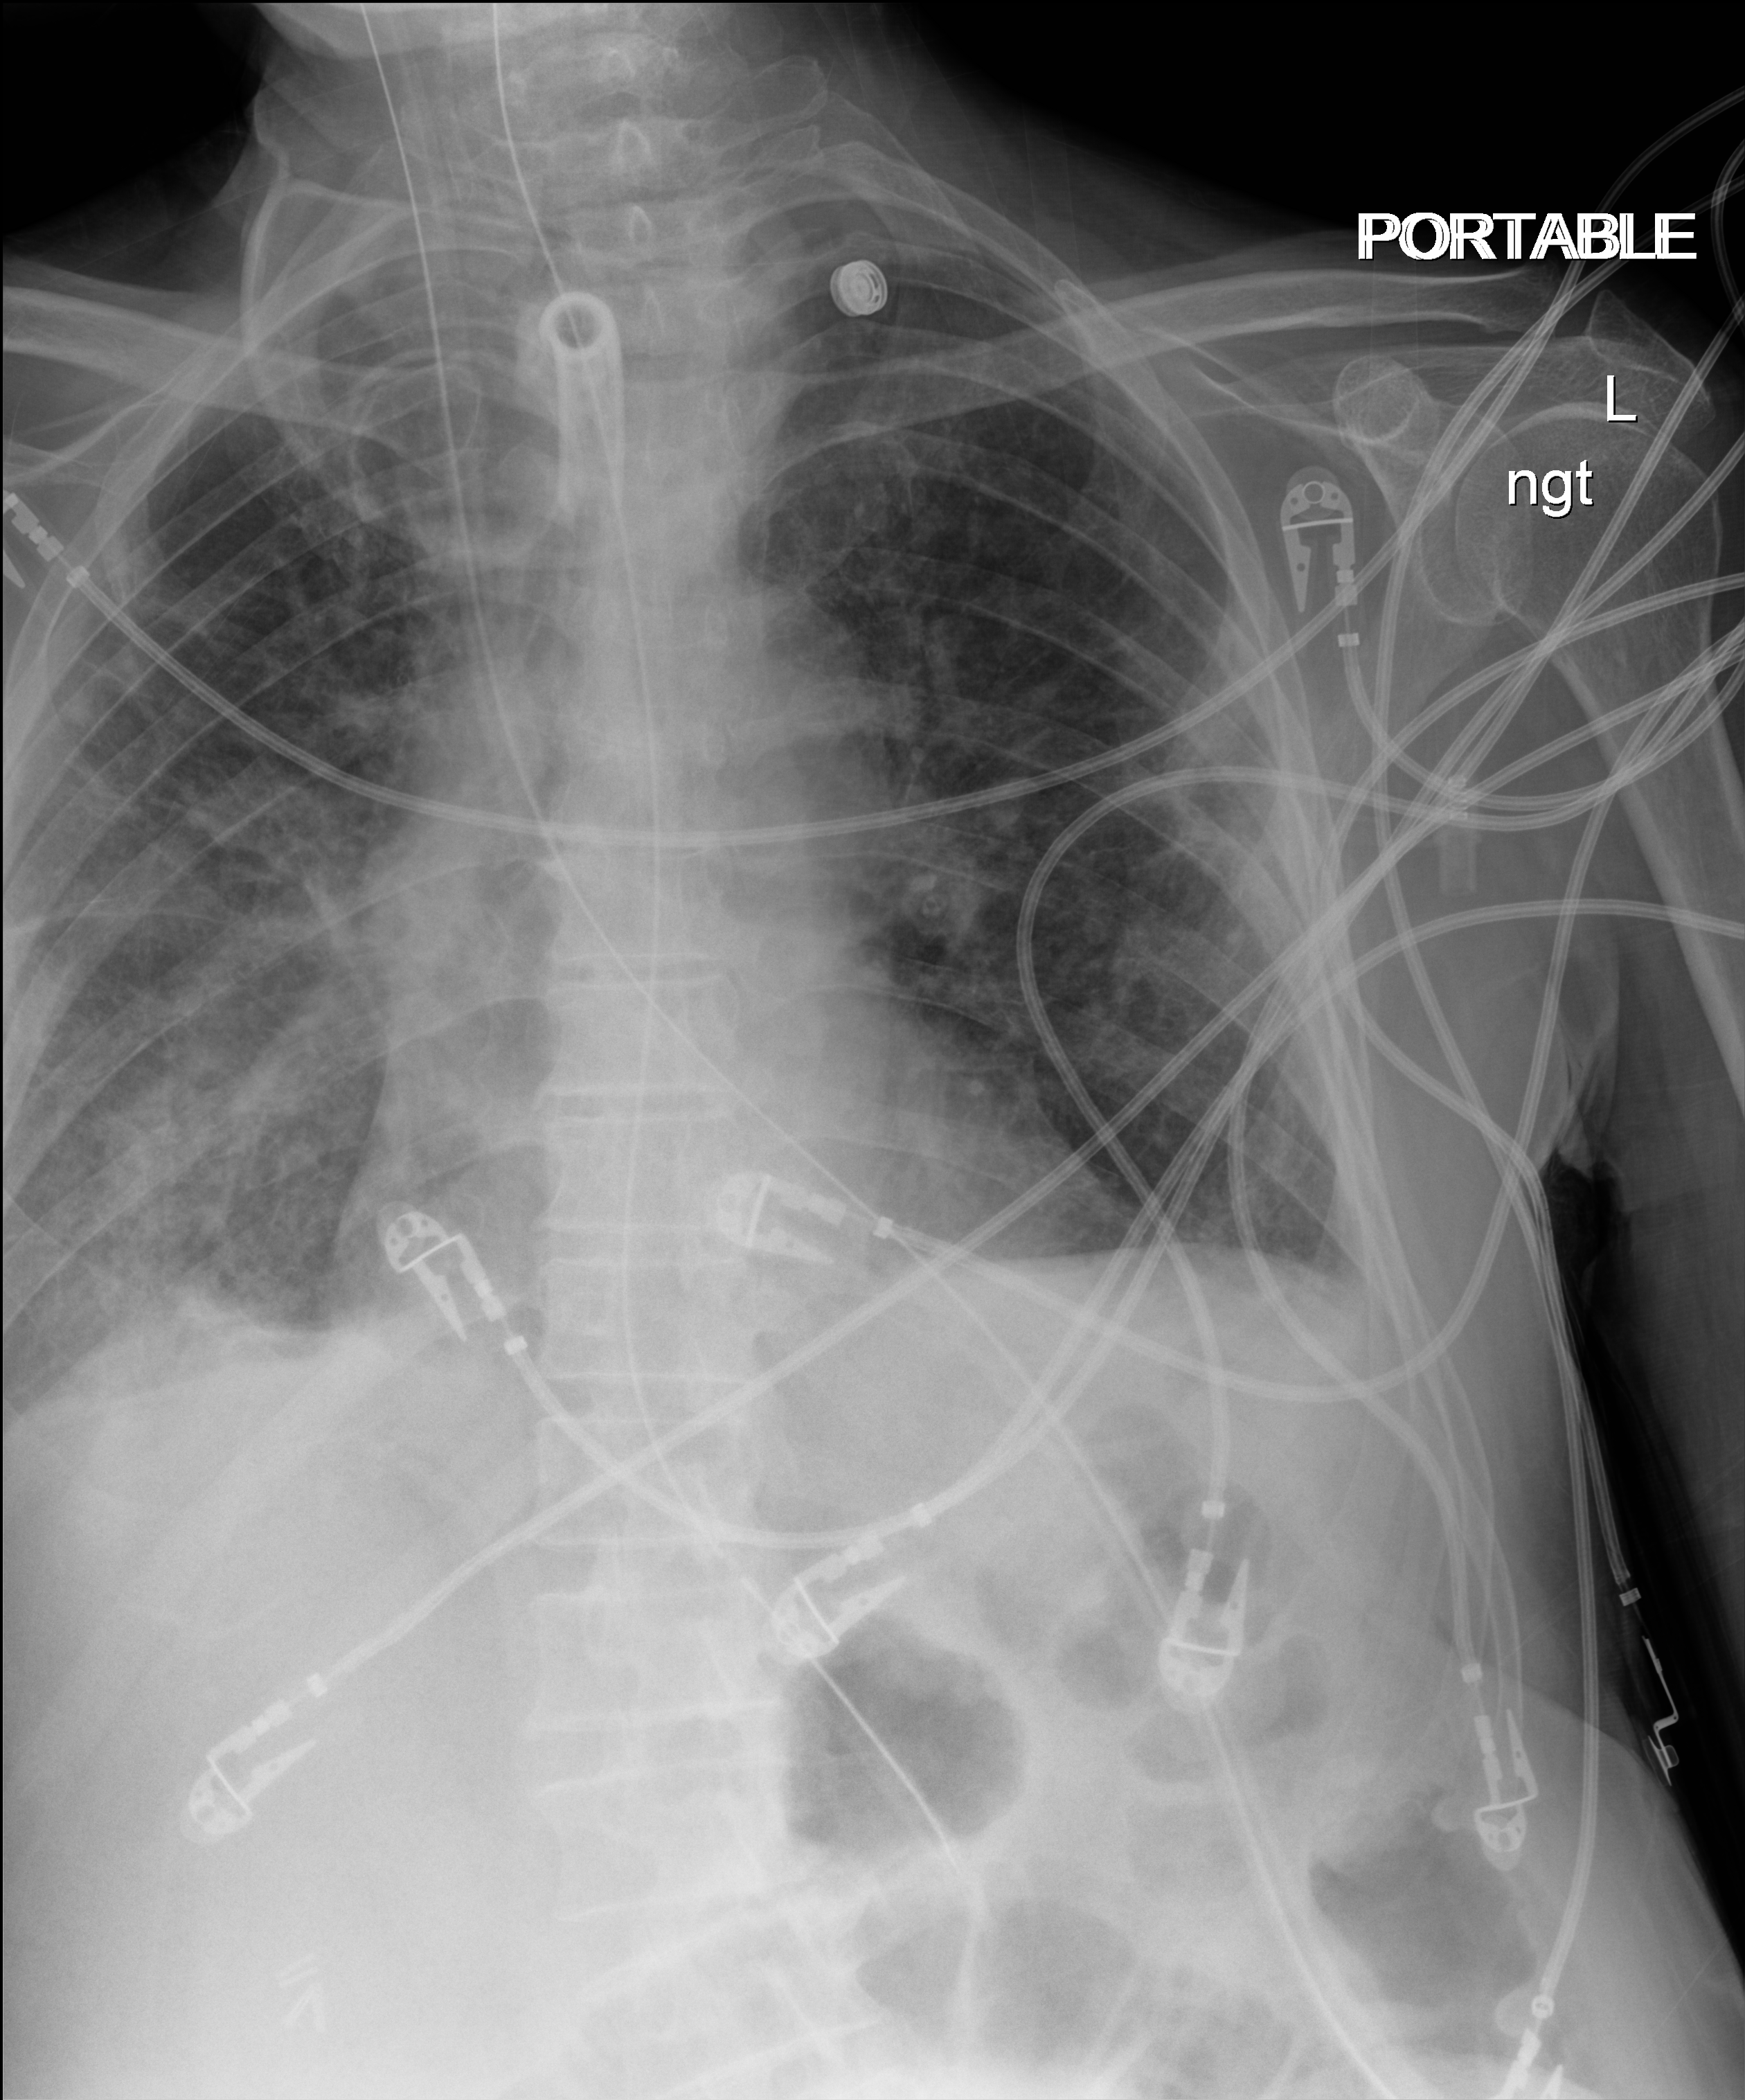
Bedside chest radiograph (digital radiography). Male patient hospitalised with COVID-19, age 75–90 years.
Hospital-stay facts (about this admission, not read from this image; timing relative to this image not recorded): admitted to intensive care during this hospital stay: yes; mechanically ventilated during this hospital stay: yes; chronic kidney disease (admission record): no.